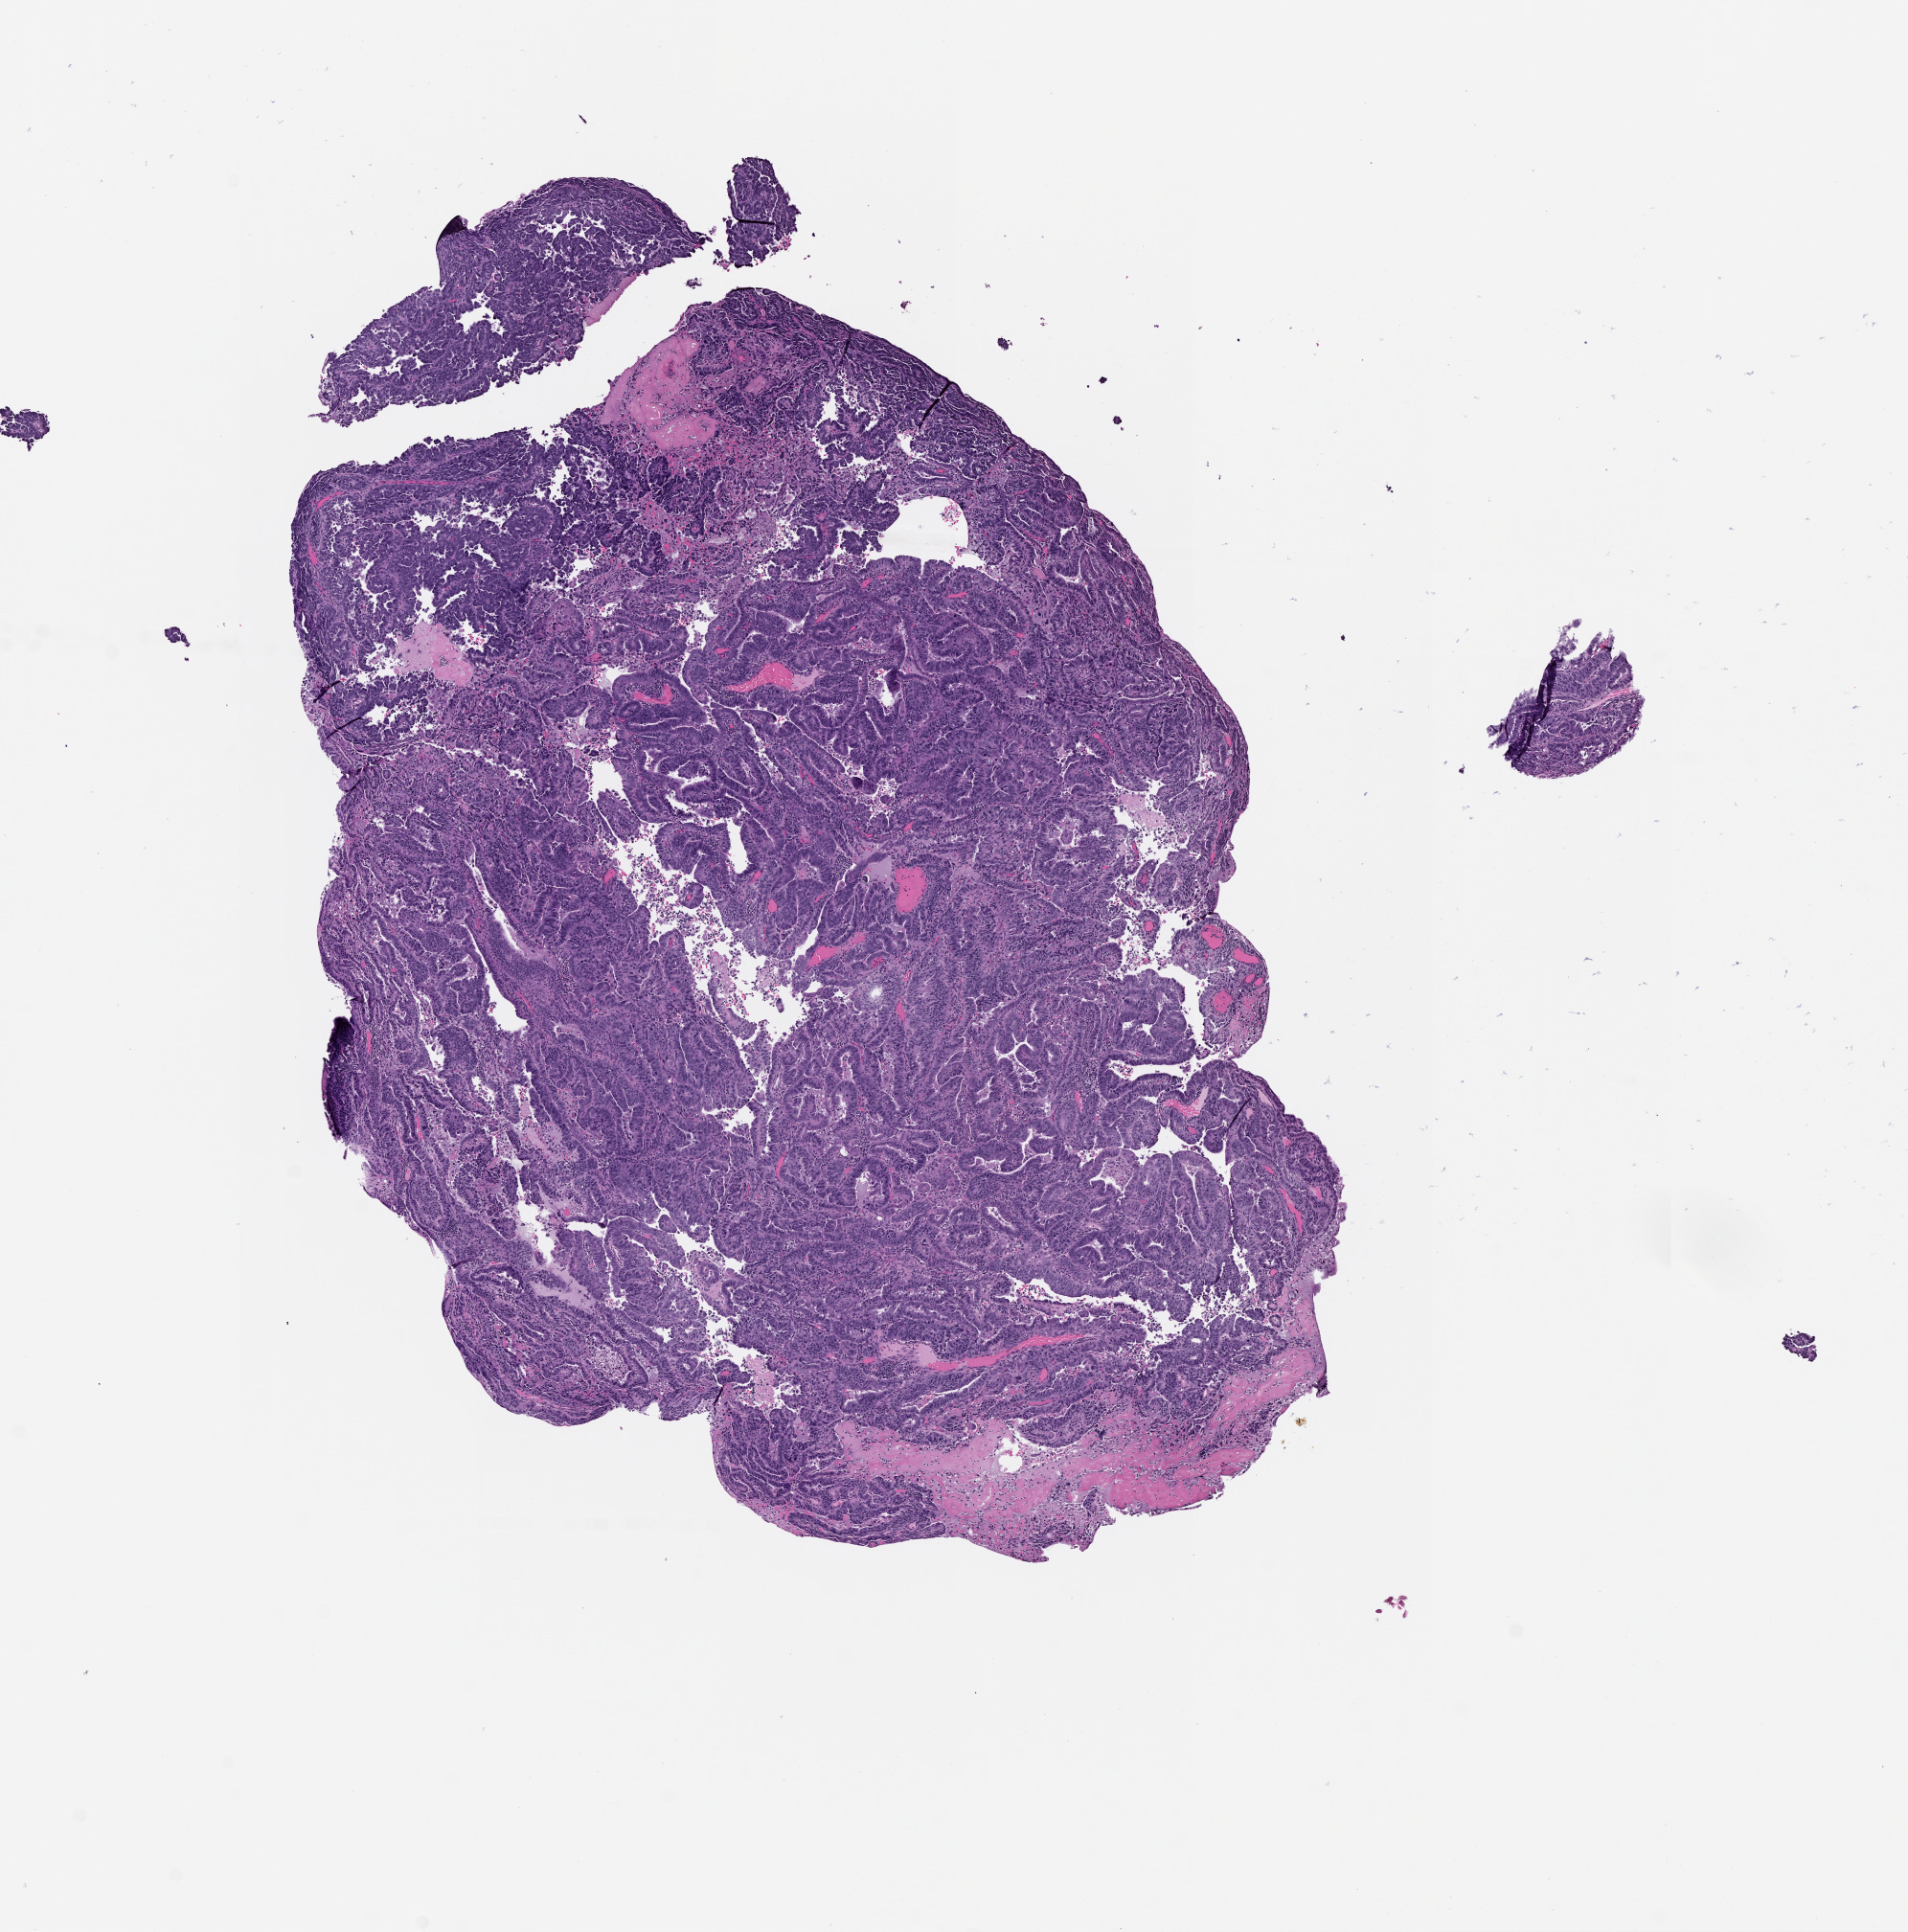
H&E-stained whole-slide image — a low-resolution overview of the entire scanned area, about 8.0 x 8.1 mm; uterus, tumour tissue. Female, 58 y/o. Histologic grade: G3 (poorly differentiated).
AJCC pathologic stage: IIIC1. Diagnosis: Endometrioid adenocarcinoma, NOS. Primary tumour site (as recorded): posterior endometrium.